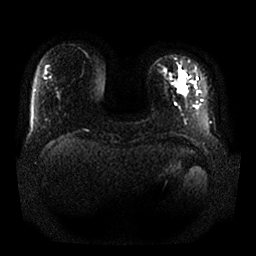
Breast MRI, one axial slice. Position 2 of 25 along the scan axis. Diffusion-weighted series; image 2 of 4 stored at this slice position (different b-values; order by instance number). 1.5 T. 4 mm slice thickness. 256 × 256 image matrix, field of view 380 × 380 mm. Female patient.
Outlined on this slice (manually delineated by an expert):
- tumour on diffusion-weighted imaging: bounding box <177,77,185,94> (left, top, right, bottom; pixels)